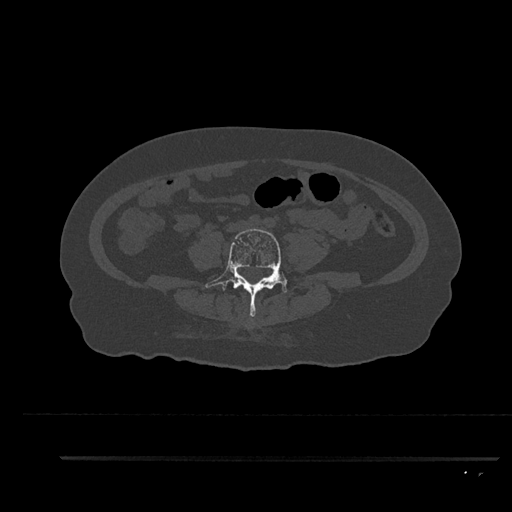
CT including the spine, one axial slice; slice 21 of 797 in the series (ordered by position); reconstruction kernel Br40s/3; 120 kVp; bone window (W 1800 / L 400 HU); 512 × 512 image matrix, field of view 408 × 408 mm. Patient: female, 44 years. Case-level facts recorded for this patient, not image findings: primary cancer: renal.
Structures marked on this image (semi-automatic segmentation, software-assisted and operator-edited):
- L4 vertebra: bounding box (x1, y1, x2, y2) in pixels: (206, 228, 287, 317)